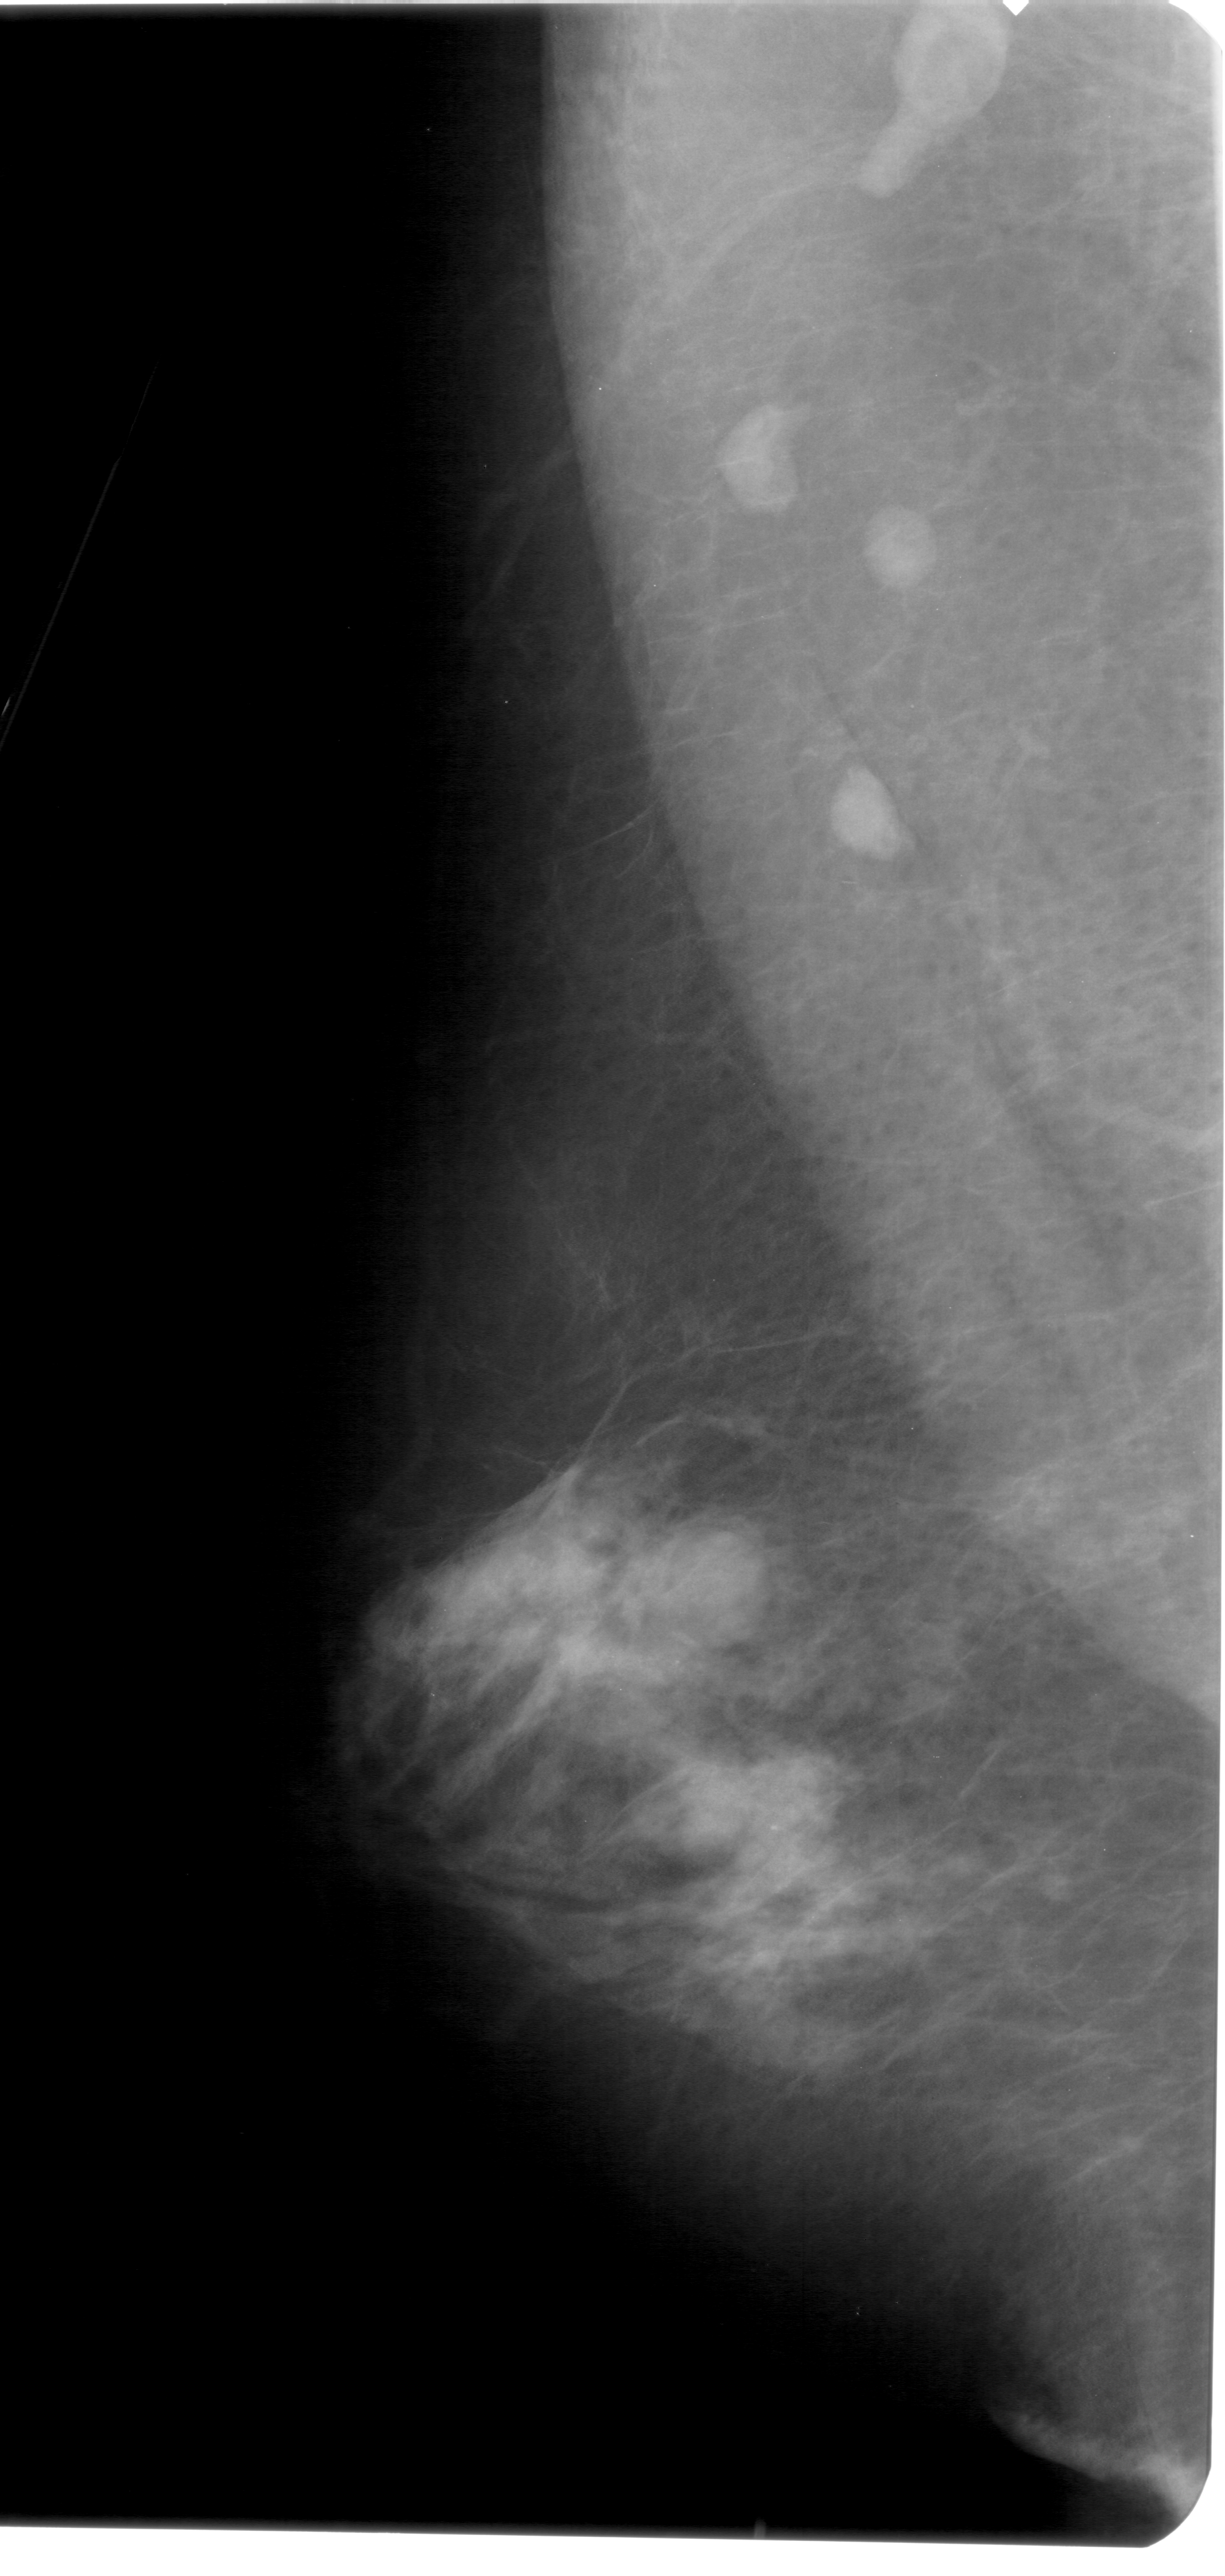
Scanned film-screen mammogram; left breast; mediolateral oblique (MLO) view; breast composition: extremely dense (BI-RADS density category 4 of 4); 1225 × 2576 image matrix.
Expert-marked regions of interest on this film, with their recorded descriptors:
- mass, shape round, margins circumscribed; BI-RADS assessment category 4; subtlety rating 3 on a 1 (subtle) to 5 (obvious) scale; pathology (as recorded): benign: bounding box (x1, y1, x2, y2) in pixels: (587, 1515, 759, 1658)